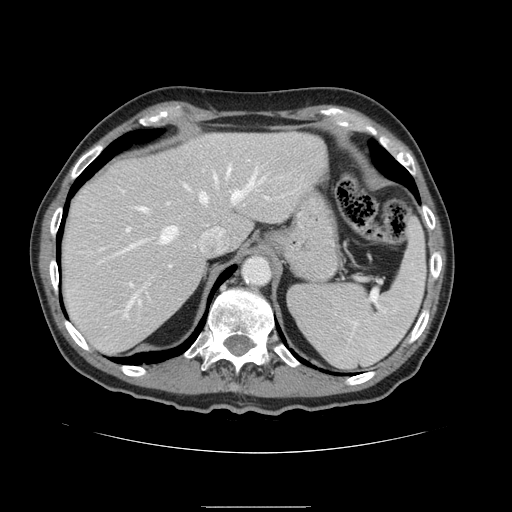
Contrast-enhanced abdominal CT, one axial slice. Intravenous contrast given. Soft-tissue window (W 400 / L 40 HU). 2.5 mm slice thickness. 512 × 512 image matrix, field of view 386 × 386 mm. Male patient, age 74 years. From the clinical record (not read from this slice): diagnosis: colorectal cancer liver metastases, imaged before liver resection; multiple liver metastases: no; largest metastasis: 14.5 cm; chemotherapy before resection: no.
Annotated regions visible in this slice (manually delineated by an expert):
- hepatic veins: bounding box [x1, y1, x2, y2] px = [118, 162, 283, 304]
- liver: [62, 132, 327, 355]
- planned liver remnant (the part of the liver to remain after resection): [62, 132, 327, 354]
- portal vein (with intrahepatic branches): [120, 197, 270, 286]